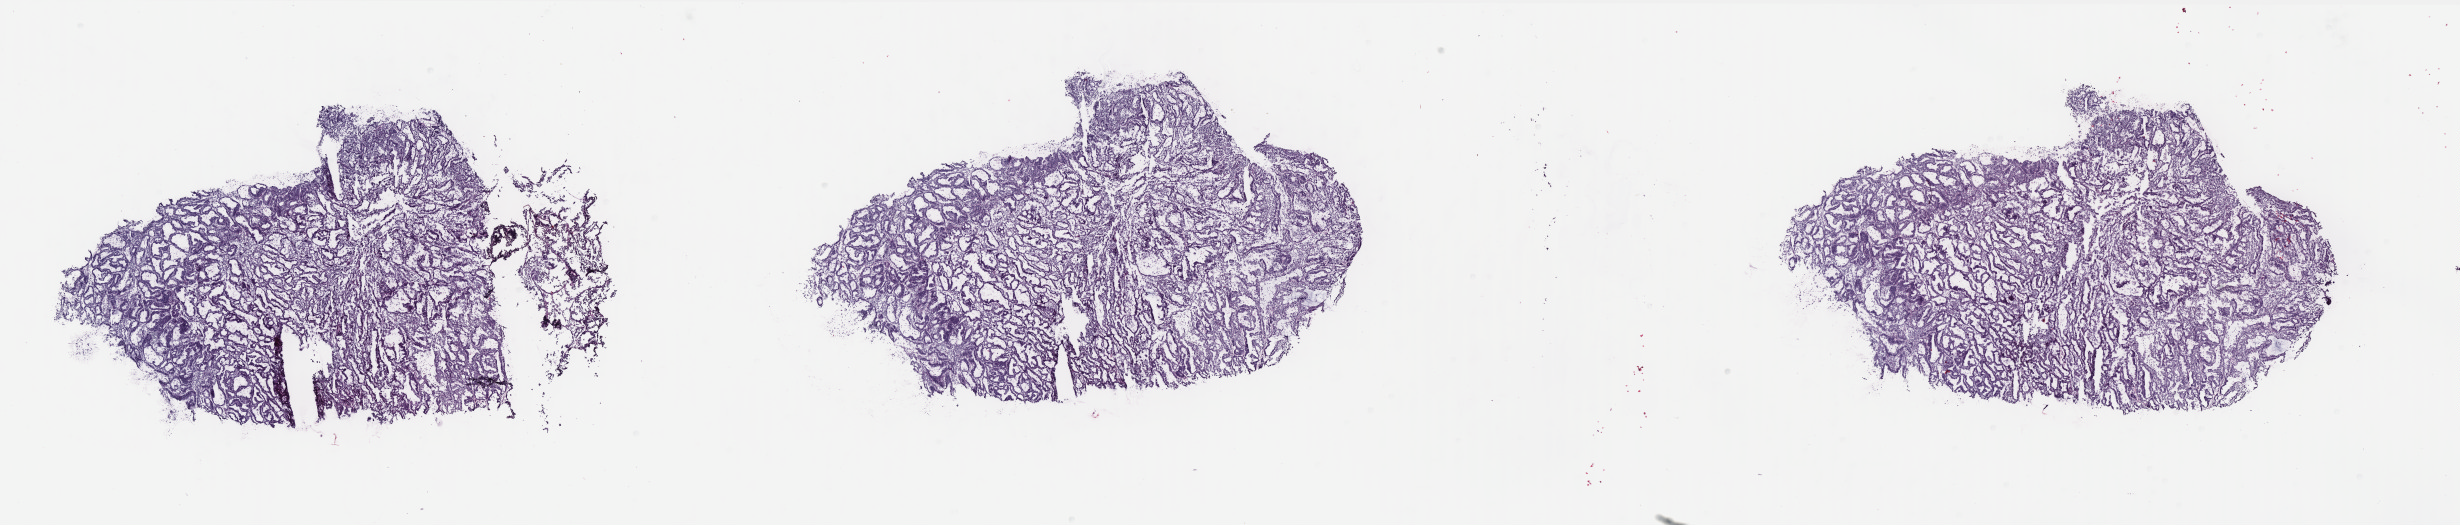
Whole-slide histology image, H&E-stained — low-resolution overview of the scanned area, about 39.4 x 8.4 mm (from a 40x scan), frozen section from the top of the tissue portion, uterus, primary tumour sample. Patient: female, age at initial diagnosis 75 years. Histologic grade: G2 (moderately differentiated). Slide review estimates, as recorded: tumour cells 100%, tumour nuclei 80%, normal cells 0%, stromal cells 0%, necrosis 0%. Inflammatory infiltration, as recorded: lymphocyte infiltration 0%, monocyte infiltration 0%, neutrophil infiltration 0%.
Pathologic diagnosis: Endometrioid adenocarcinoma, NOS (endometrium). FIGO stage: IA. Lymph nodes positive (case pathology): 0 of 3 examined.